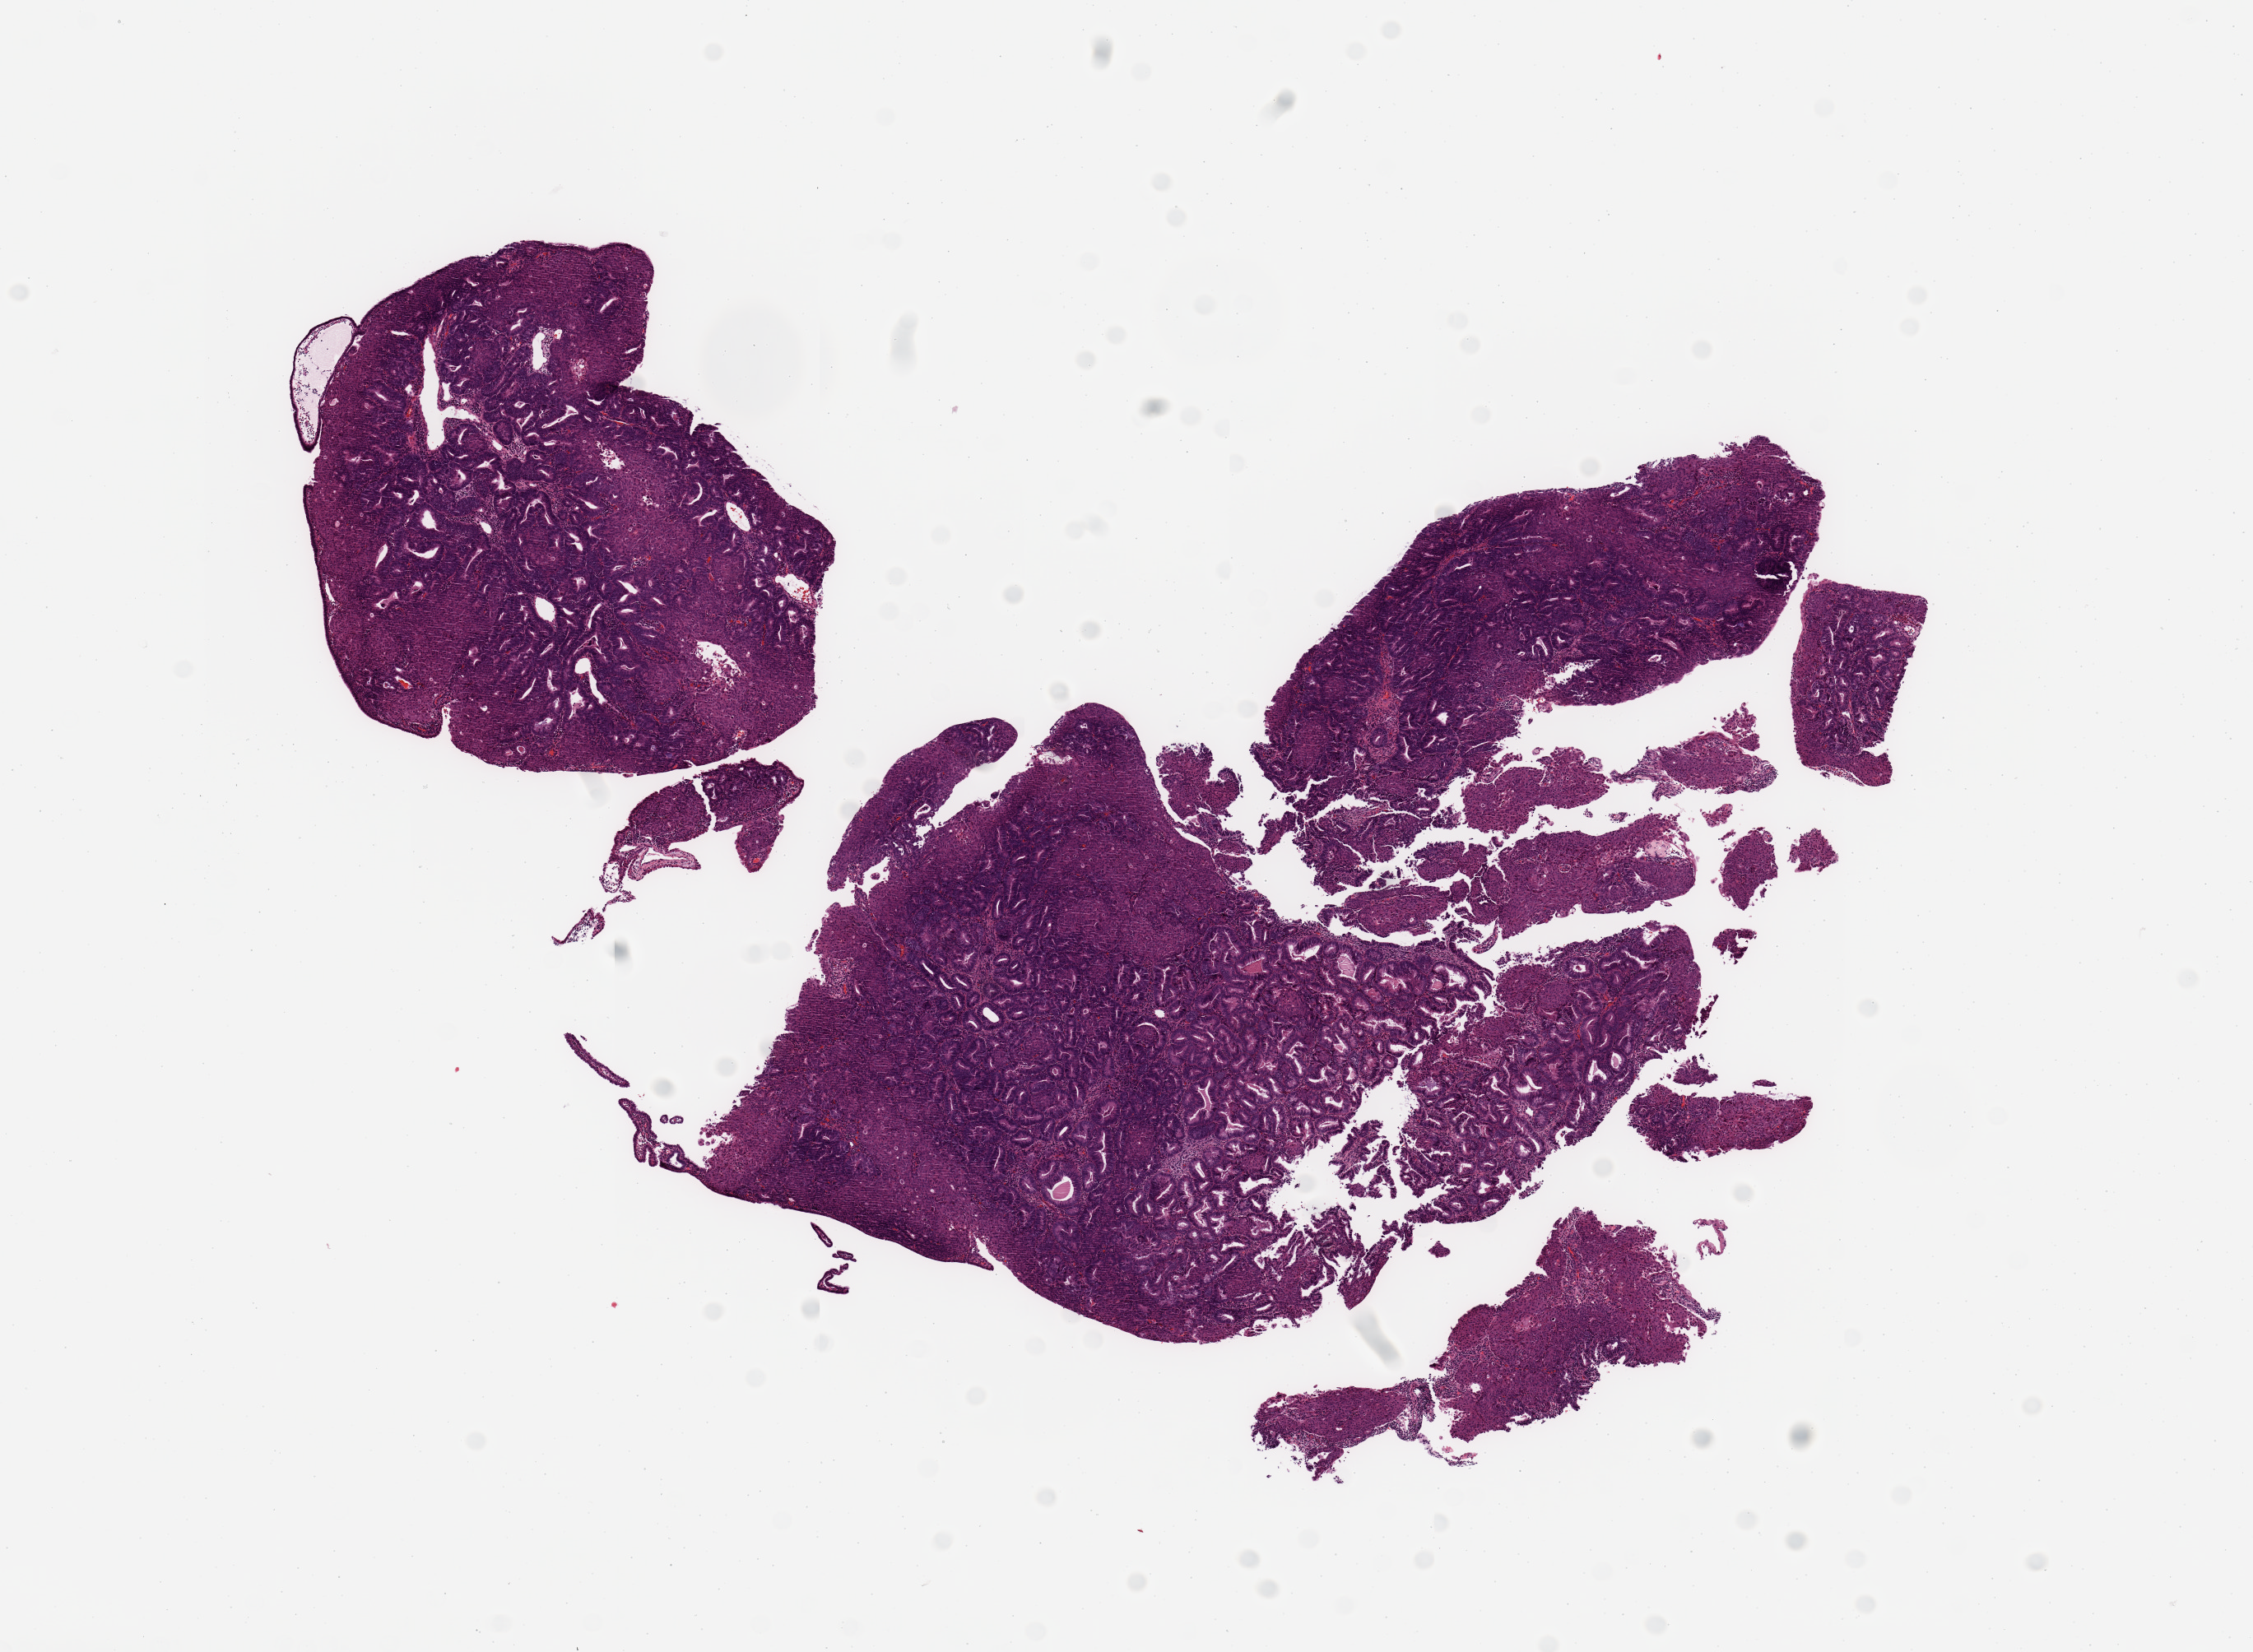
Digitized H&E tissue section (whole slide) — low-resolution overview of the scanned area, about 10.8 x 7.9 mm (slide scanned at 20x). Tumour tissue sample, sampled site: uterus. Patient: female, age 50 years. Histologic grade: G1 (well differentiated). Pathologist review of this section (percent, as recorded): tumour nuclei 98%, necrosis 2%.
AJCC pathologic stage: I. Diagnosis: Endometrioid adenocarcinoma, NOS.